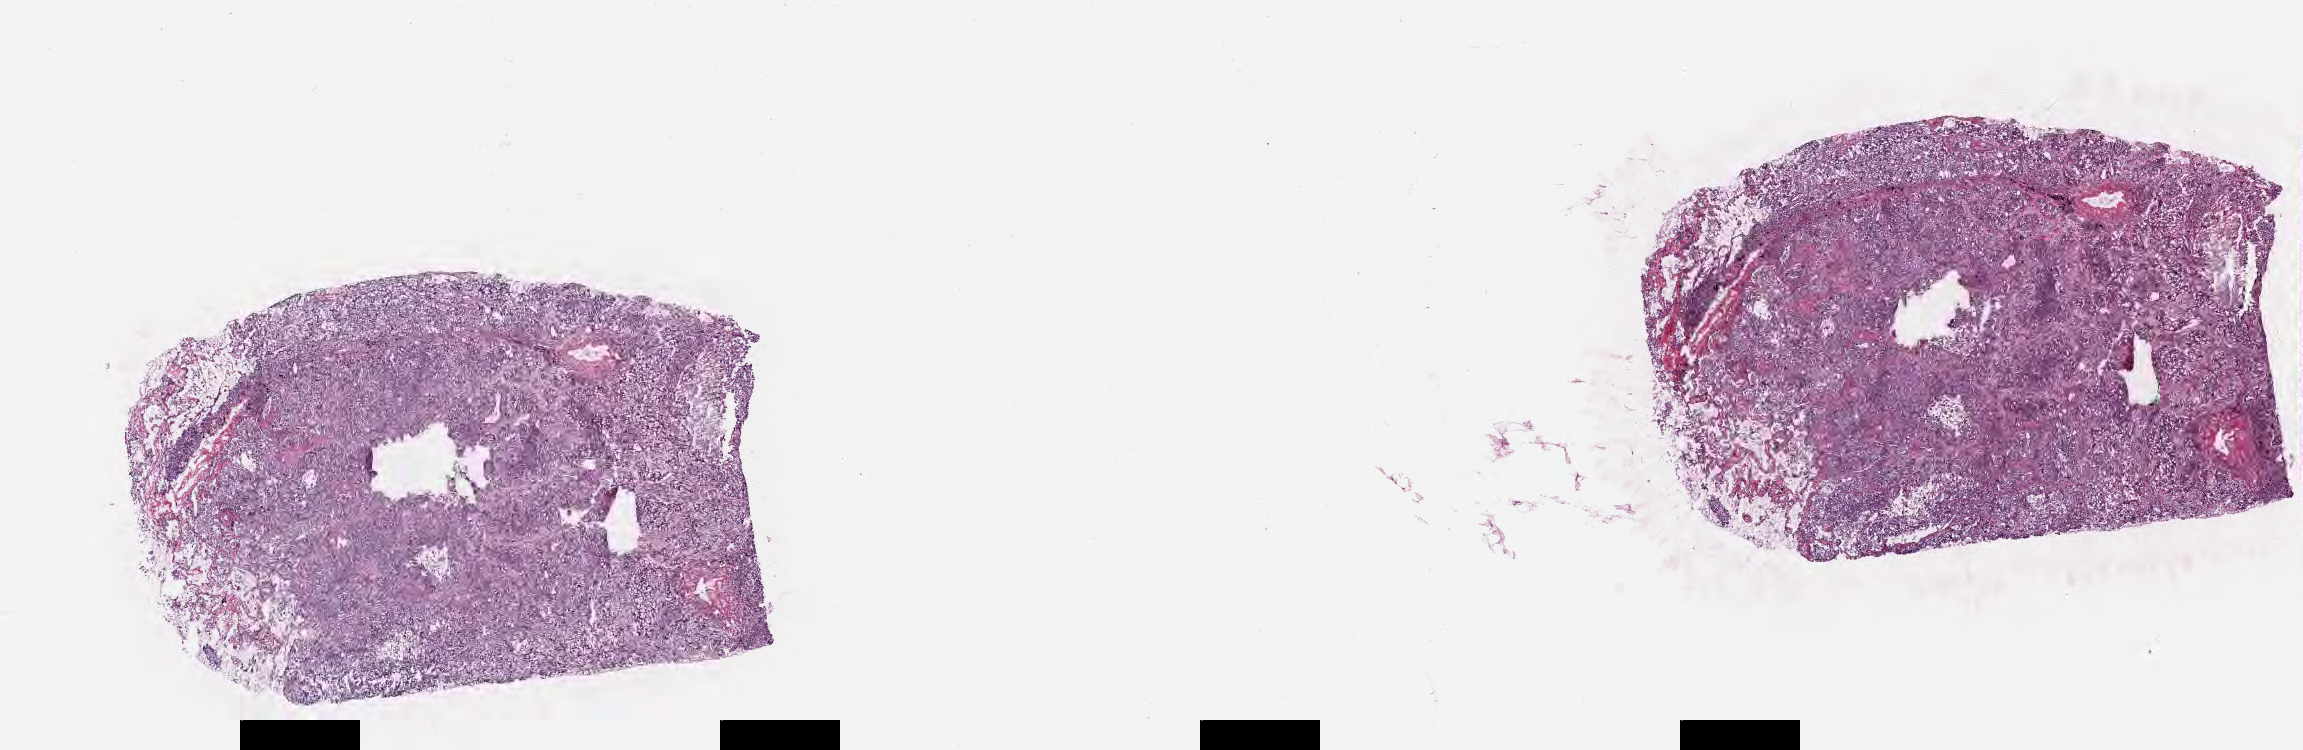
Digitized hematoxylin and eosin (H&E)-stained section, low-resolution overview of the scanned area, about 18.6 x 6.1 mm. Cryosection. Primary tumor. Site: lower lobe of right lung. Female patient, age 44 years. Composition of this section per pathologist review: tumor cells 70%, tumor nuclei 70%, stromal cells 15%, necrosis 5%, normal cells 10%. Infiltration values recorded for this section: lymphocyte infiltration 5%, monocyte infiltration 2%, neutrophil infiltration 1%.
Section: top of the tissue portion. AJCC pathologic stage: Stage IV. Histologic diagnosis: Adenocarcinoma, NOS.